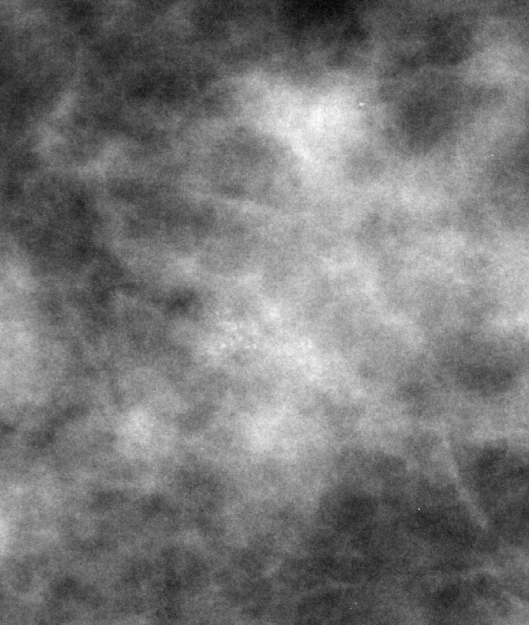
Crop from a digitized film mammogram around one marked abnormality, right breast, CC view, BI-RADS breast density category 2 (scale 1–4).
Finding: calcifications, morphology amorphous, distribution clustered; BI-RADS assessment category 4; subtlety rating 2 on a 1 (subtle) to 5 (obvious) scale; pathology result (as recorded, not read from the image): benign.